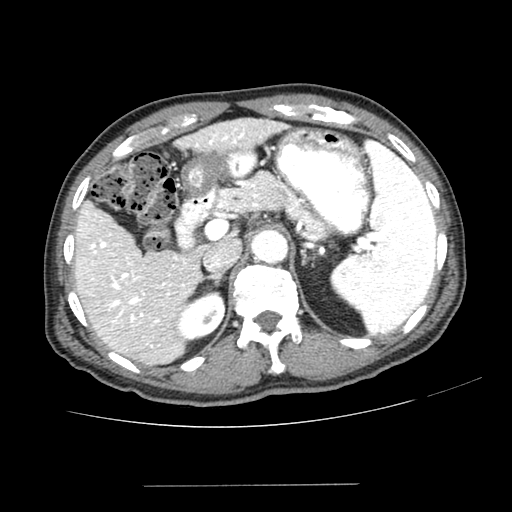
Contrast-enhanced abdominal CT (liver protocol), one axial slice; position 152 of 187 along the scan axis; reconstruction kernel SOFT; one of 2 acquisitions stored at this slice position; soft-tissue window (W 400 / L 40 HU); 512 × 512 image matrix, field of view 360 × 360 mm. From the clinical record (not read from this slice): diagnosis: hepatocellular carcinoma (patient treated with transarterial chemoembolisation; whether this scan precedes or follows treatment is not stated here); TNM stage (as recorded): Stage-I; Child-Pugh class: A; tumour differentiation: poorly differentiated; tumour nodularity: uninodular.
Annotated regions visible in this slice (semi-automatic segmentation, software-assisted and operator-edited):
- liver parenchyma outside the tumour (the mass and vessels are separate outlines, so this box may not span the whole liver): bounding box <74,118,280,364> (left, top, right, bottom; pixels)
- liver vessels: <79,128,244,347>